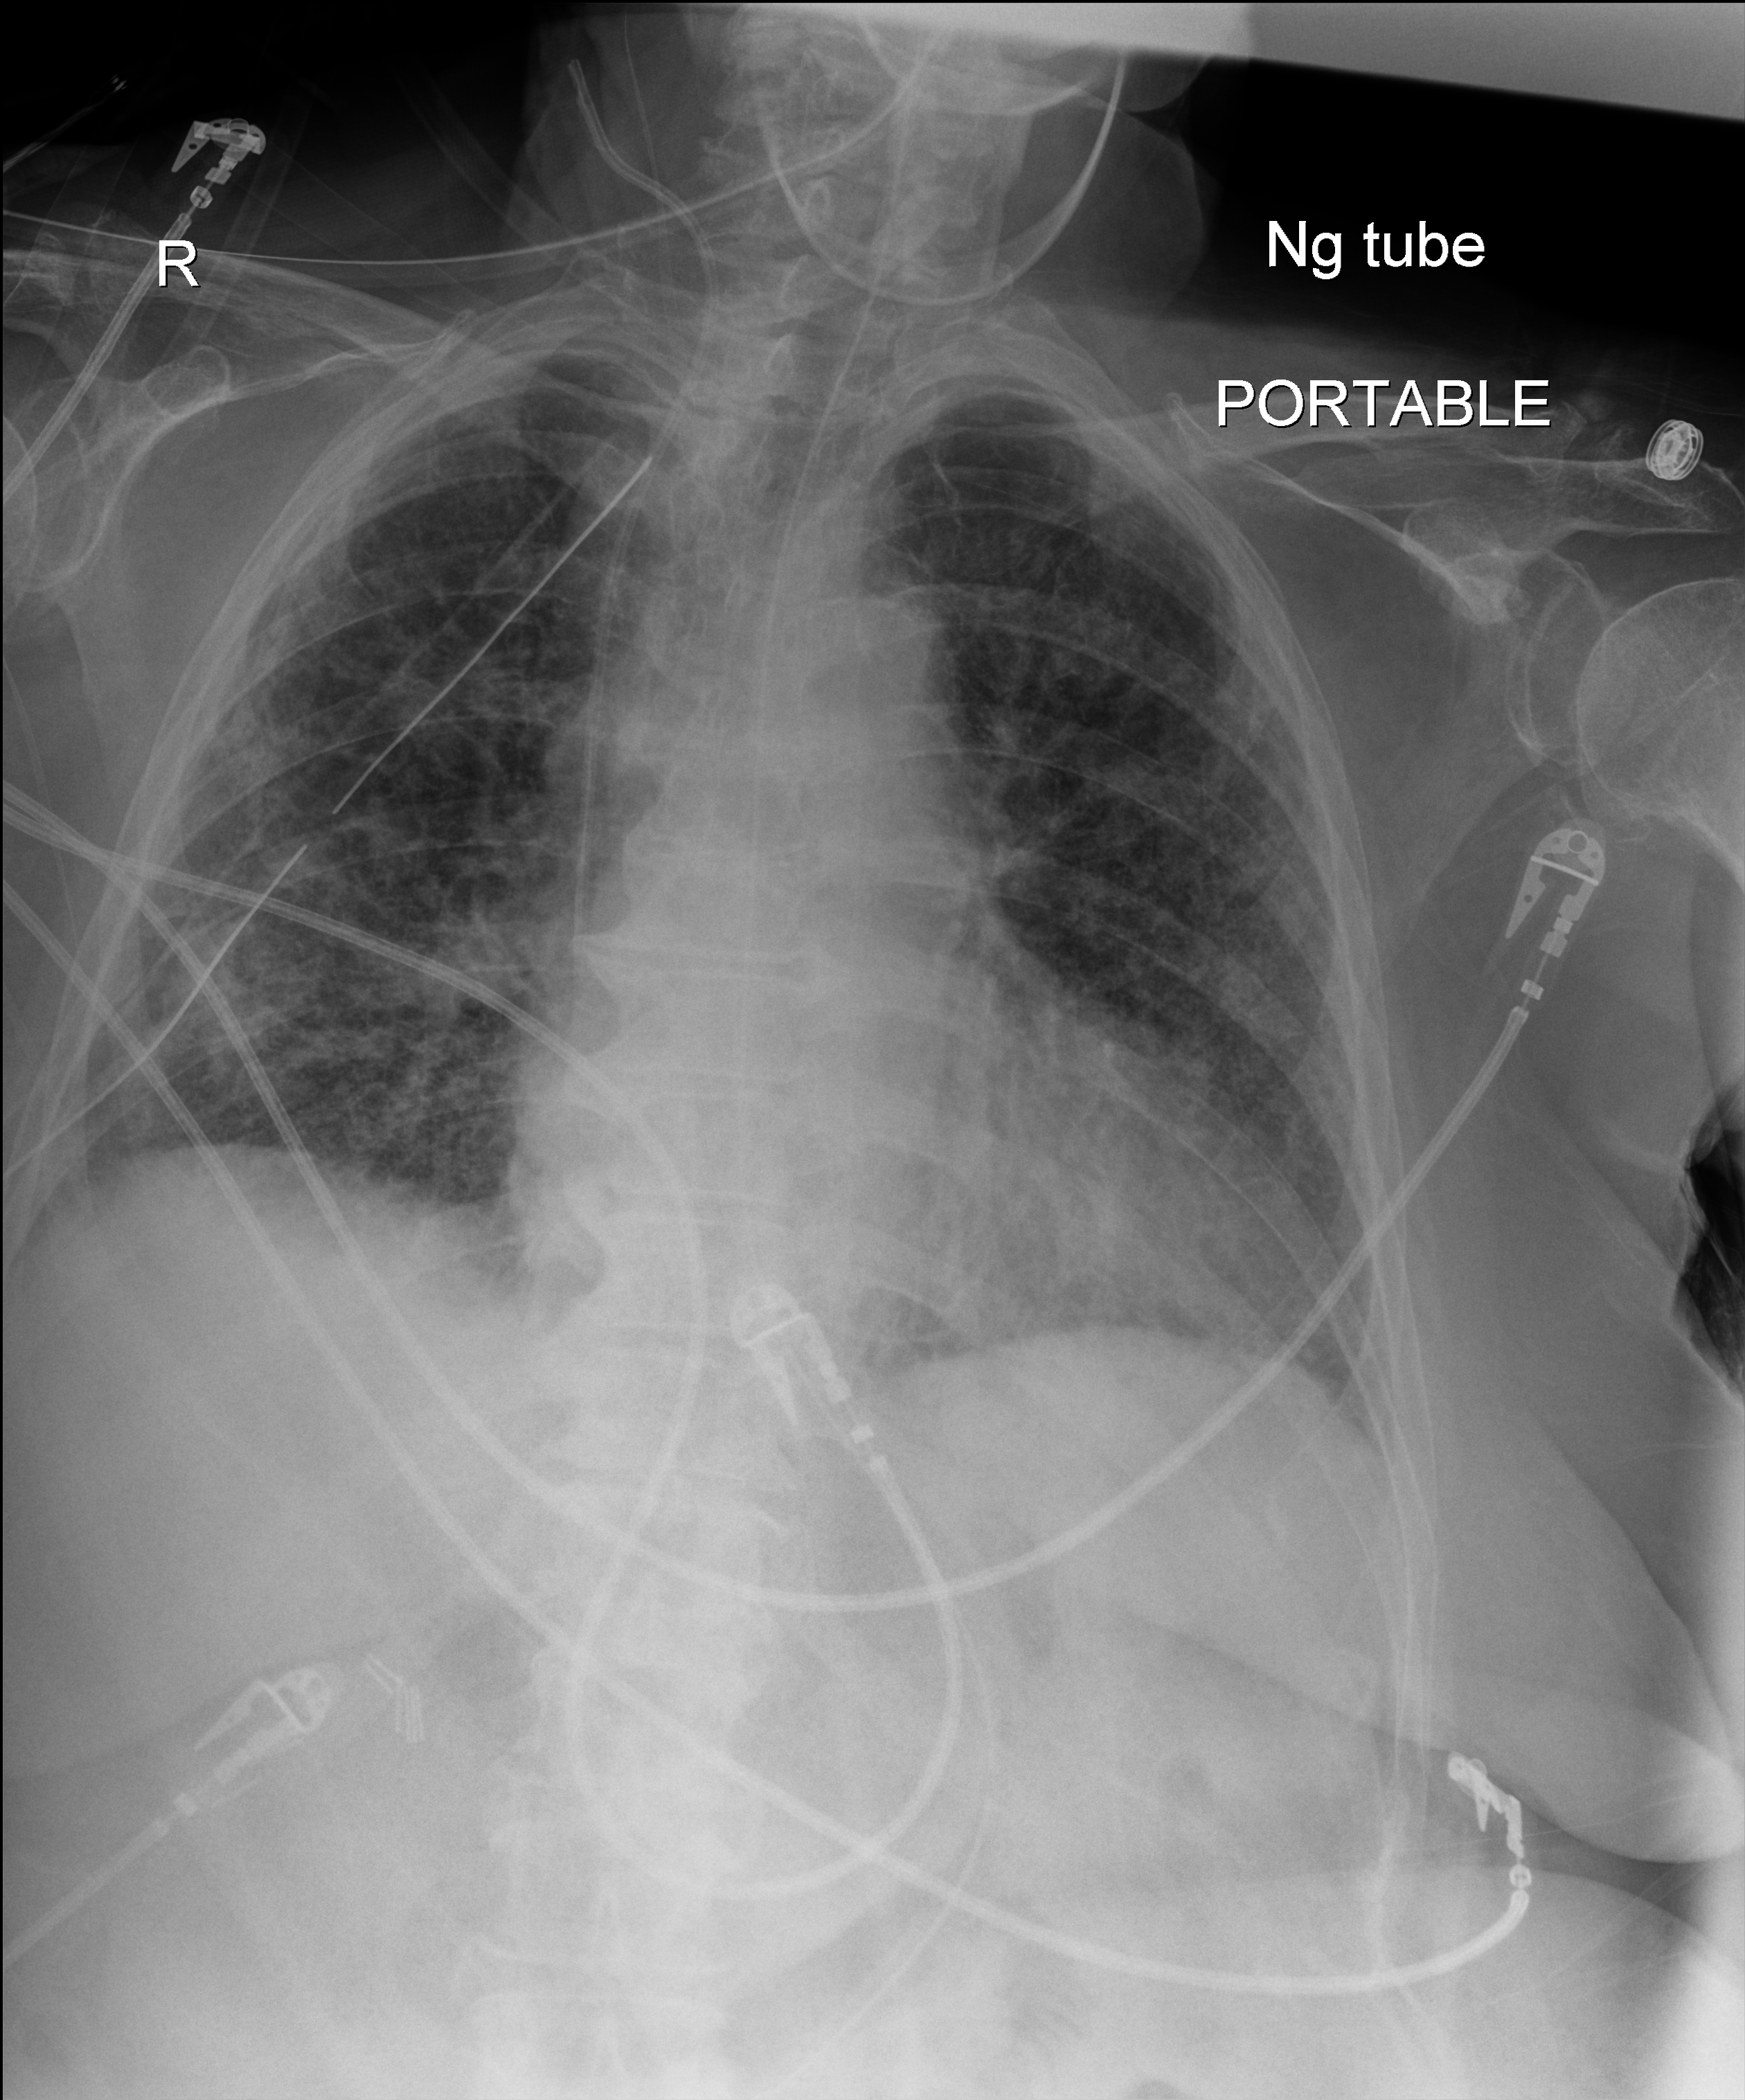
Chest X-ray (portable). Patient hospitalised with COVID-19; female, aged 75–90 years.
Admission-level facts for this patient (not findings on this image; timing relative to this image not recorded): admitted to intensive care during this hospital stay: no; other chronic lung disease (admission record): no; mechanically ventilated during this hospital stay: yes.